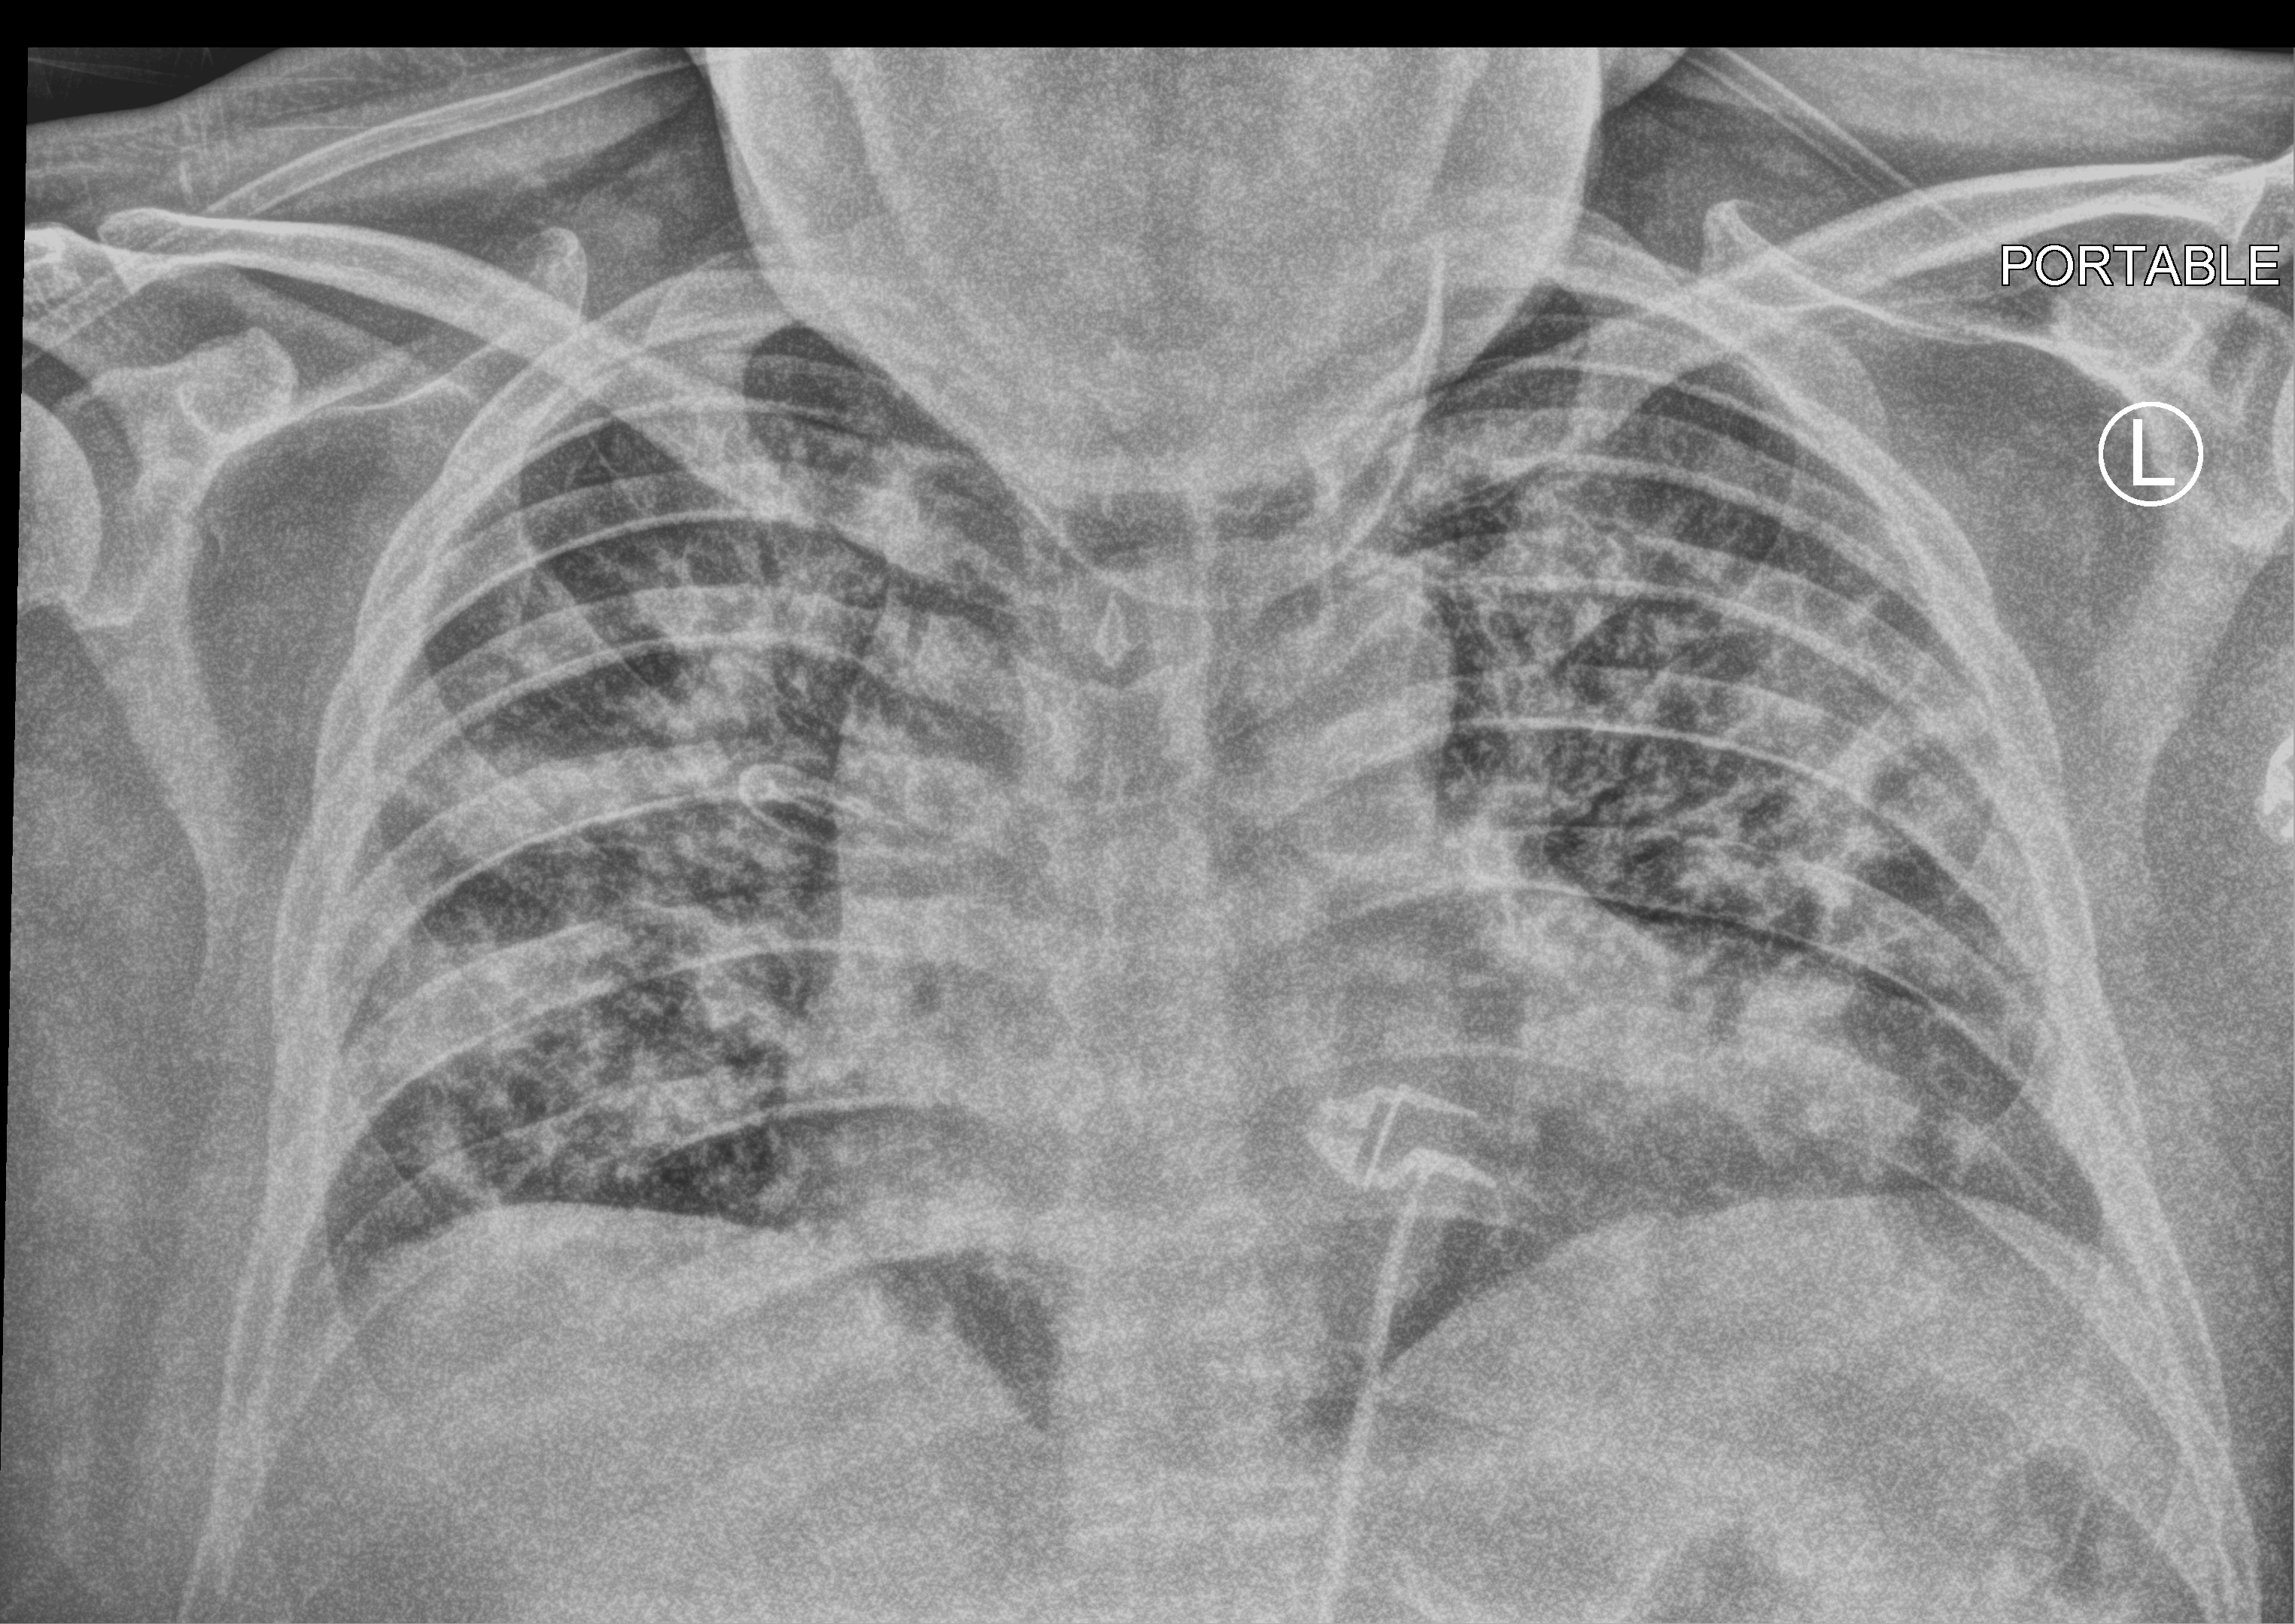
Bedside chest radiograph (computed radiography), anteroposterior (AP) projection. Male patient hospitalised with COVID-19, age 18–59 years.
Admission-level facts for this patient (not findings on this image; timing relative to this image not recorded): mechanically ventilated during this hospital stay: no; hypertension (admission record): no; admitted to intensive care during this hospital stay: no.